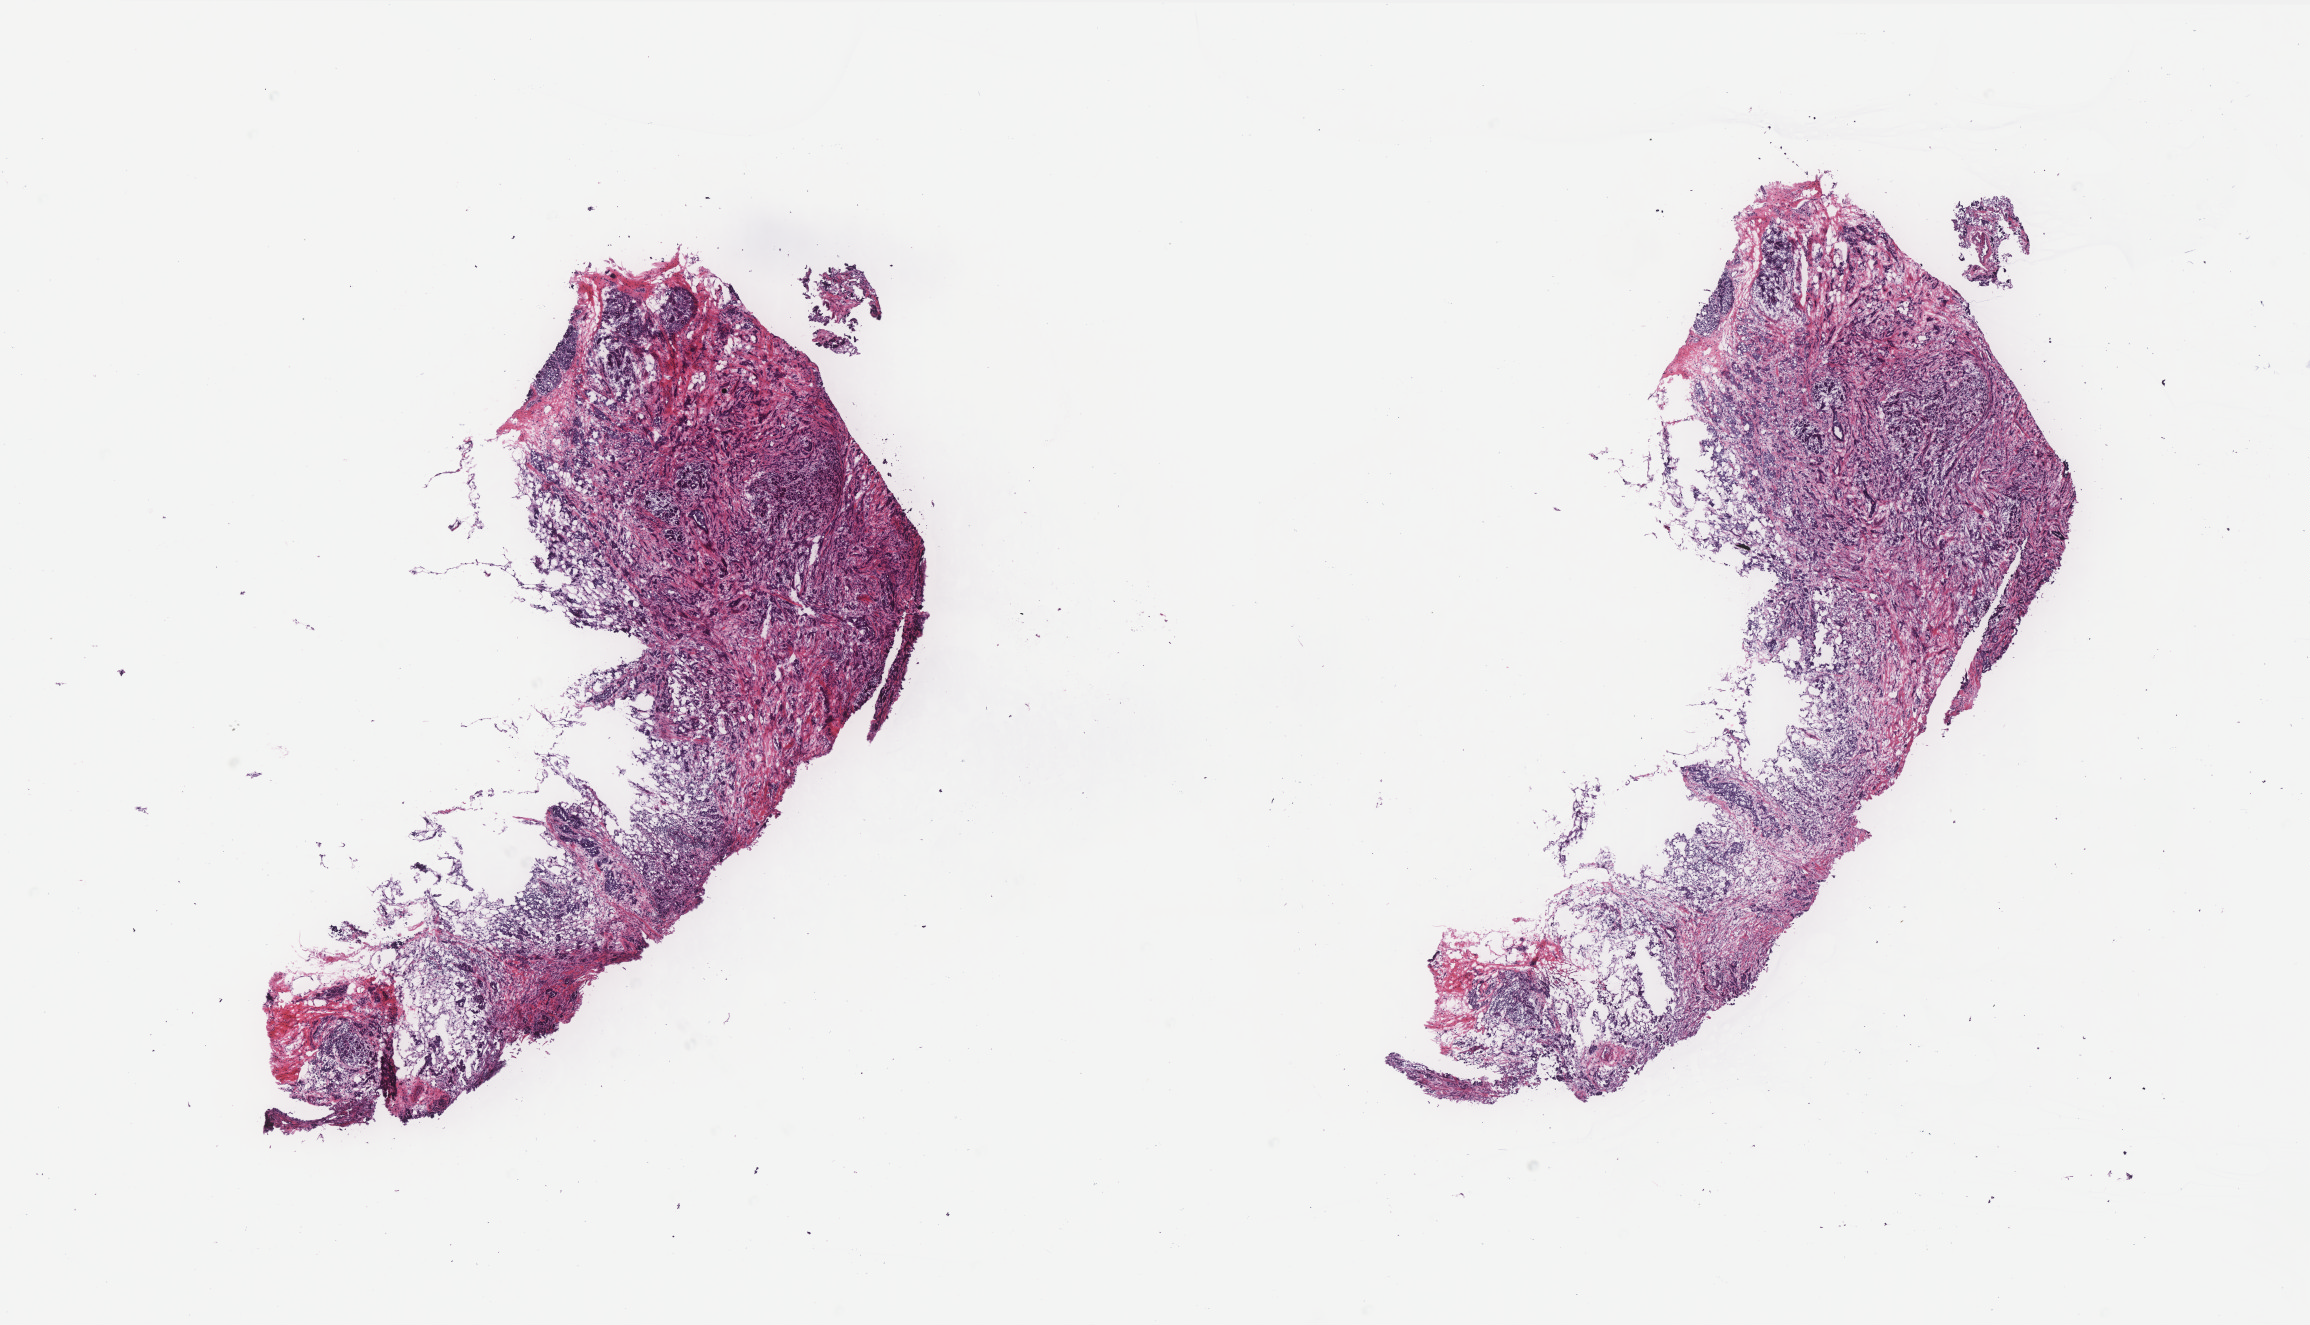
H&E-stained whole-slide image — whole scanned area (about 18.5 x 10.6 mm, from a 40x scan) shown as a low-resolution overview. Frozen section from the bottom of the tissue portion. Breast, primary tumour sample. Female, age 47 years at initial diagnosis. Slide review estimates, as recorded: tumour cells 95%, tumour nuclei 65%, normal cells 5%, stromal cells 0%, necrosis 0%. Infiltration values recorded for this section: lymphocyte infiltration 0%, monocyte infiltration 0%, neutrophil infiltration 0%.
AJCC pathologic stage: IIA (6th edition). Diagnosis: Infiltrating duct carcinoma, NOS. Lymph nodes positive (case pathology): 0 of 27 examined.